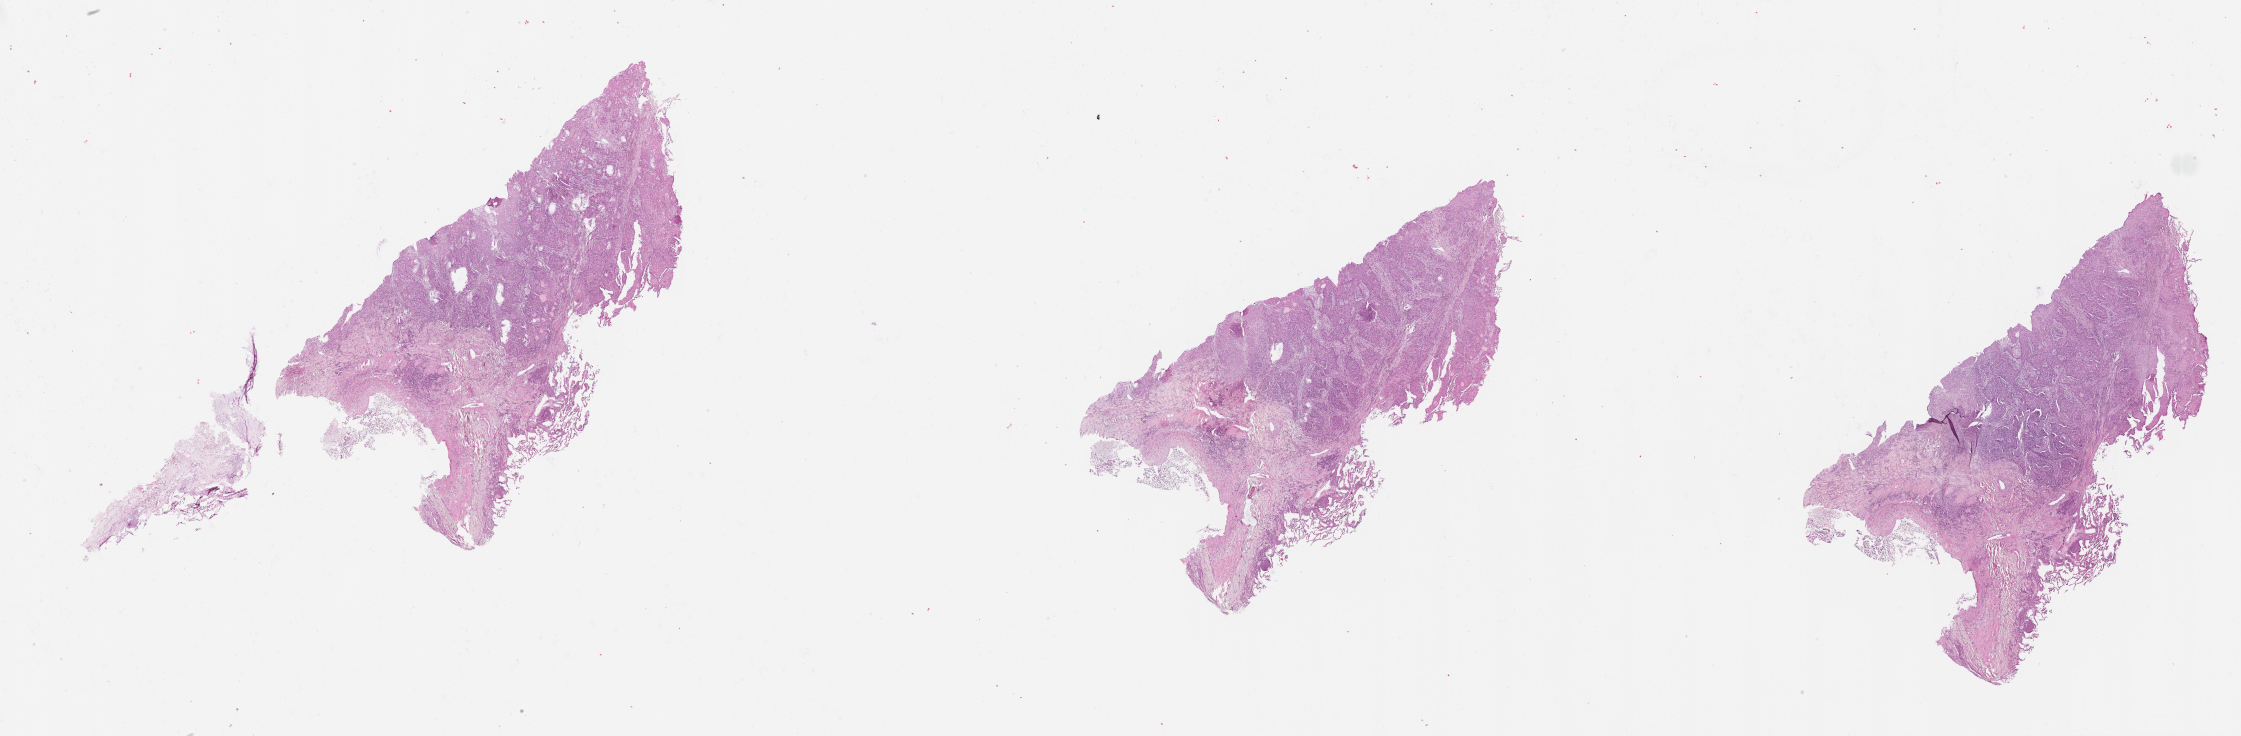
Hematoxylin and eosin (H&E) stained whole-slide image, a low-resolution overview of the entire scanned area, about 36.1 x 11.8 mm, lung, tumour tissue. Male, 53 y/o.
* patient diagnosis (cohort enrolment): squamous cell carcinoma (lung)